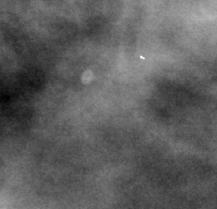
Cropped region of a digitized screen-film mammogram centred on a radiologist-marked abnormality; right breast; CC view; BI-RADS breast density category 4 (scale 1–4).
- Marked abnormality: calcifications, morphology lucent center; BI-RADS assessment category 2; subtlety rating 4 on a 1 (subtle) to 5 (obvious) scale; benign without callback (not worked up further).